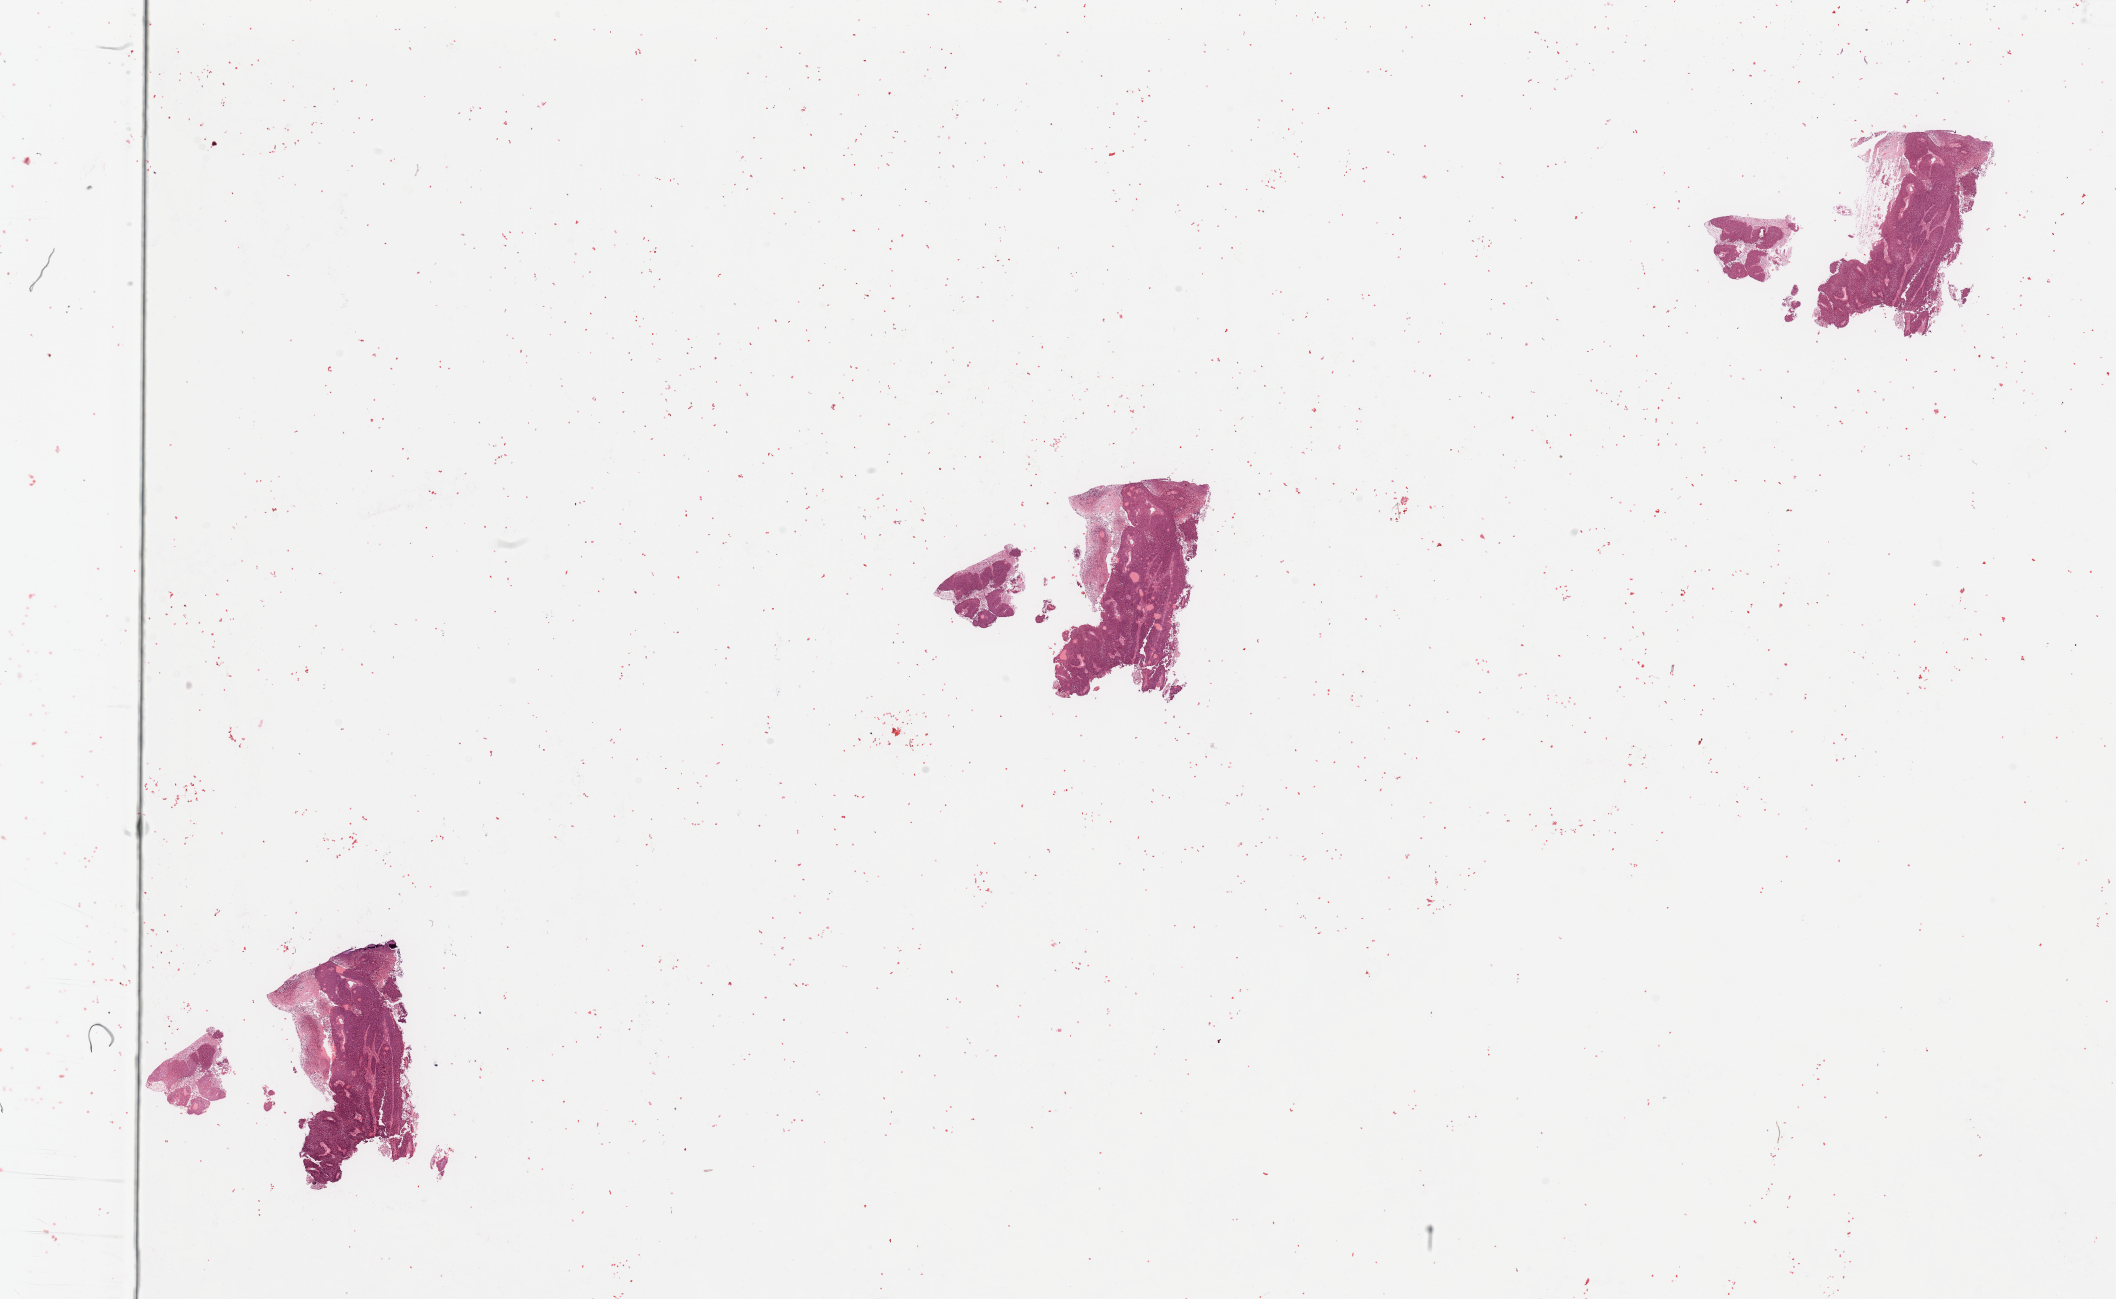
Hematoxylin and eosin (H&E) stained whole-slide image, low-resolution overview of the scanned area, about 33.5 x 20.5 mm (acquisition: 20x scan). Tumour tissue sample, sampled site: lung. Male, 69 y/o. Histologic grade: G2 (moderately differentiated). Pathologist review of this section (percent, as recorded): tumour nuclei 75%, necrosis 15%.
AJCC pathologic stage: IIB. Primary tumour site (as recorded): right lower lobe. Diagnosis: Squamous cell carcinoma, NOS.